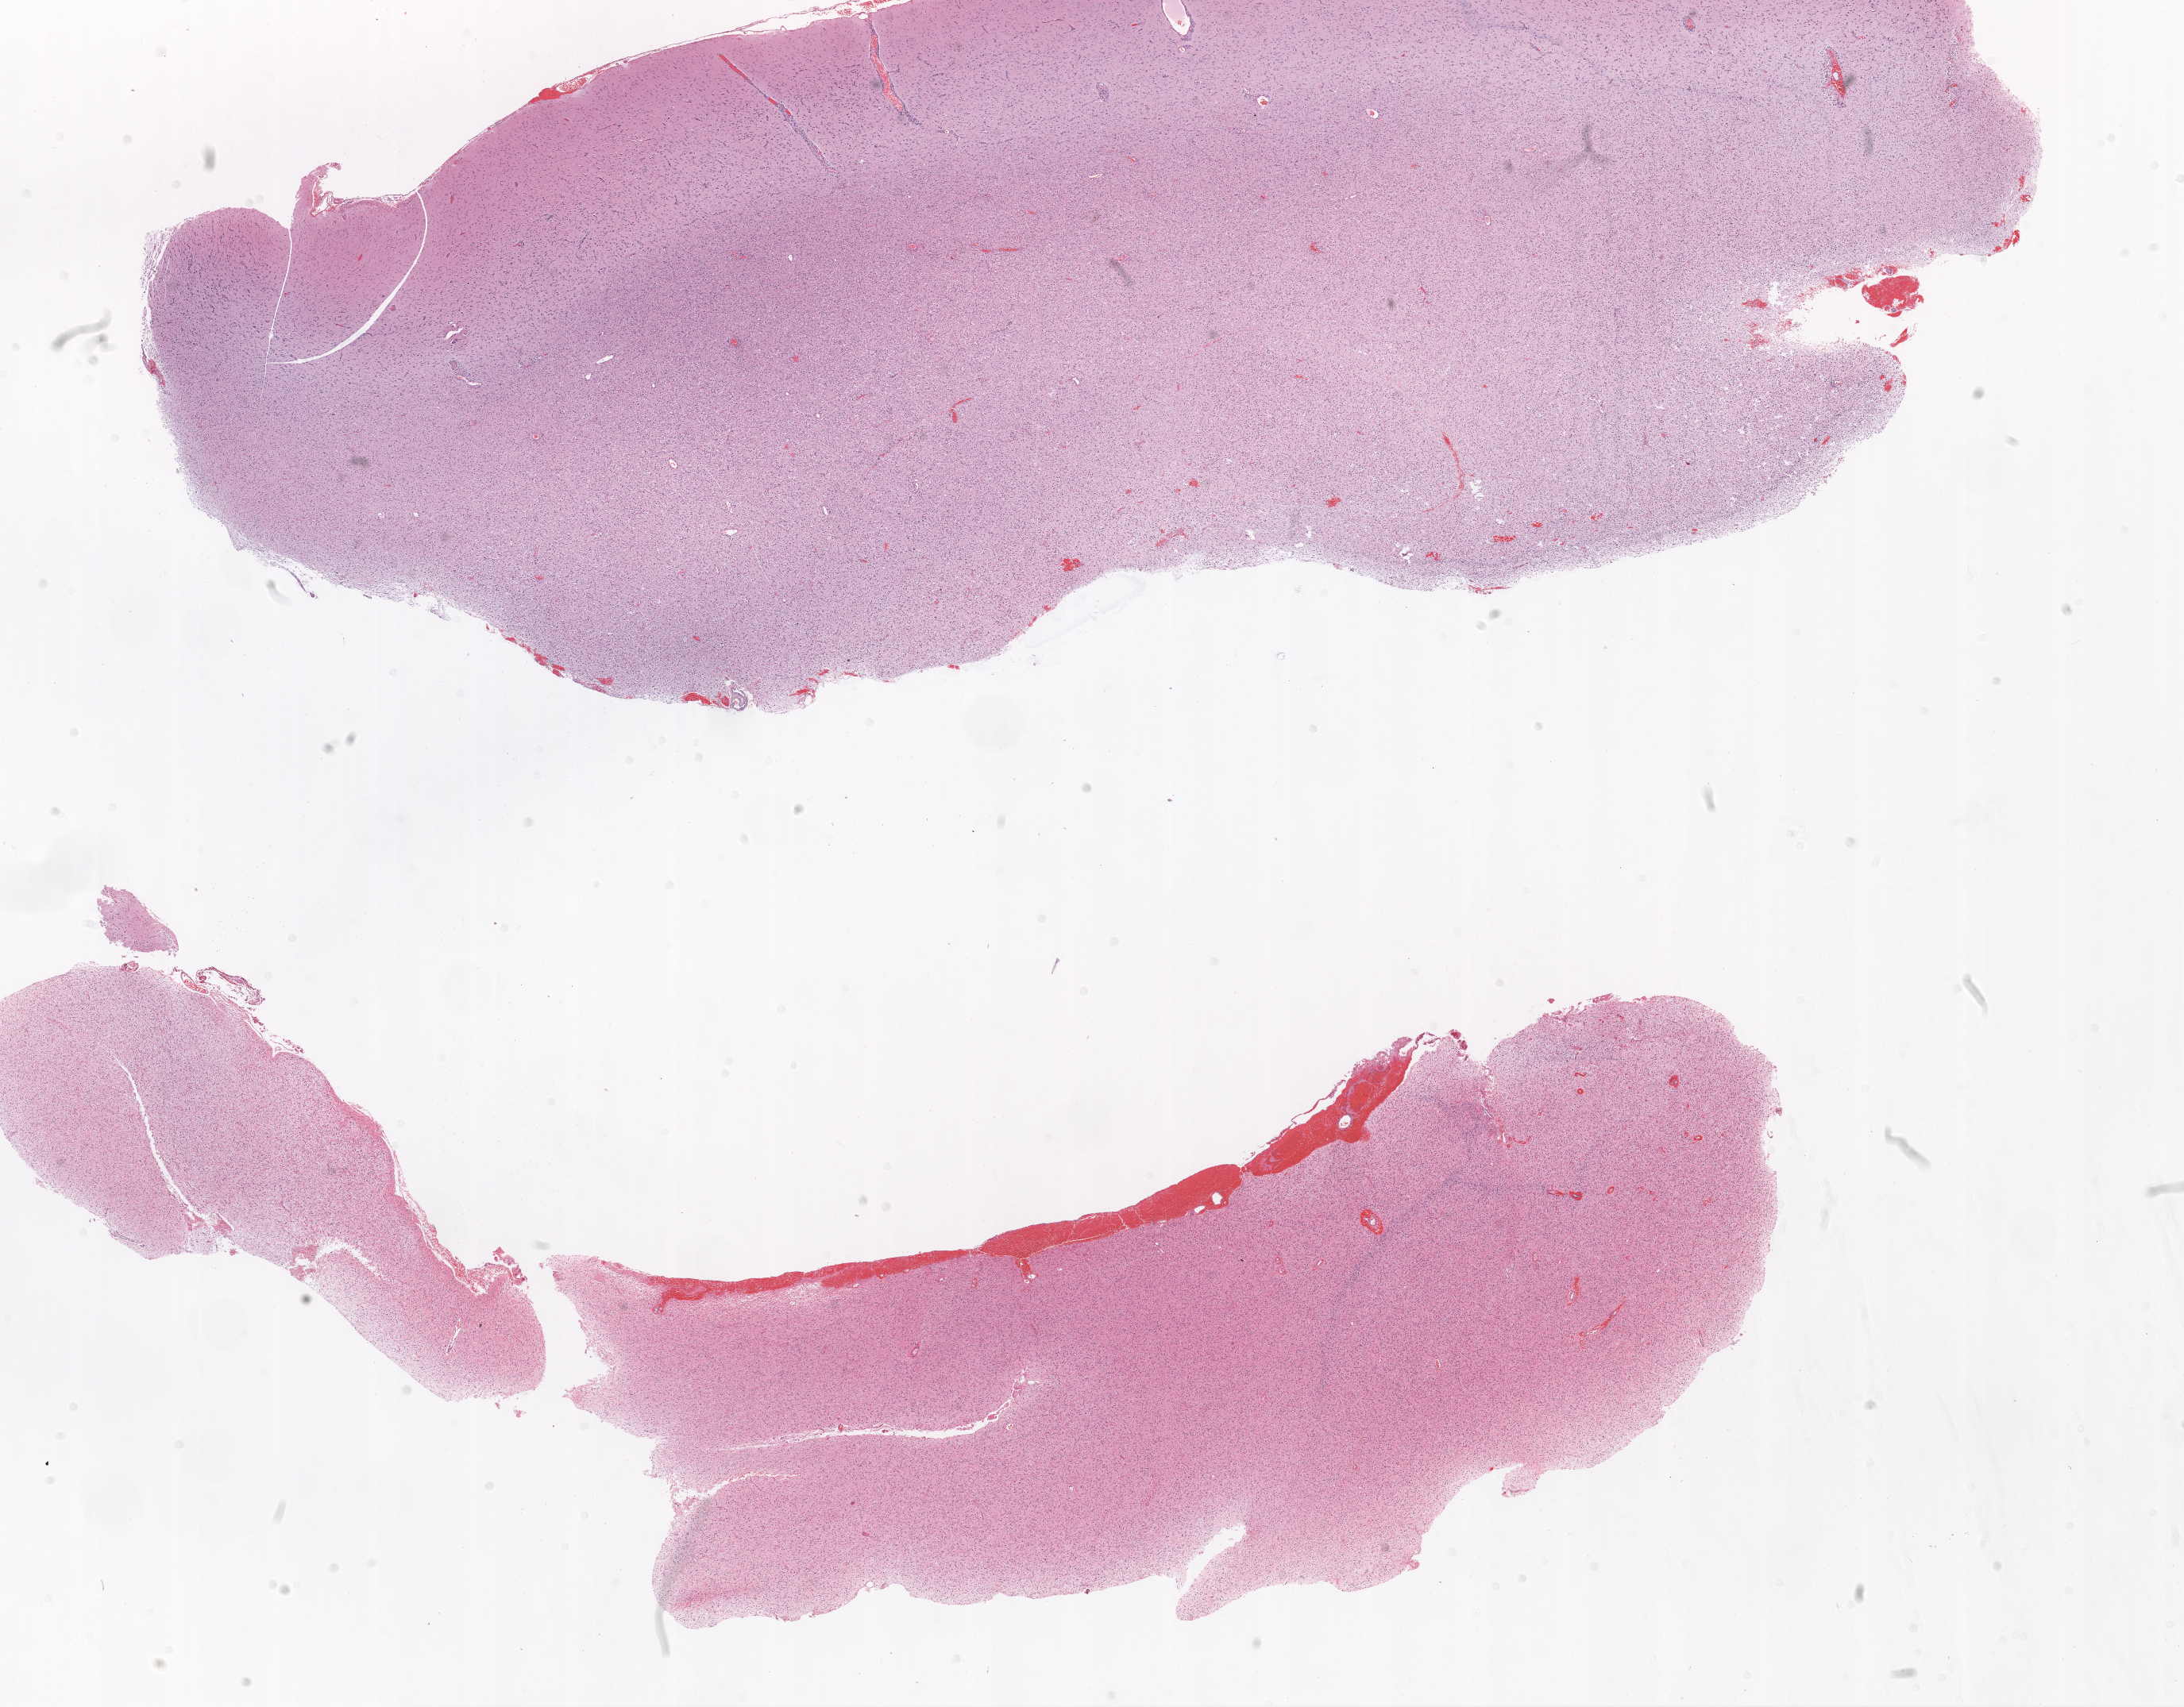
Digitized H&E tissue section (whole slide) — whole scanned area (about 22.1 x 17.3 mm) shown as a low-resolution overview. Formalin-fixed paraffin-embedded (FFPE) diagnostic section. Sample: primary tumour, brain. Patient: male, age at initial diagnosis 38 years.
Histologic diagnosis: Glioblastoma.